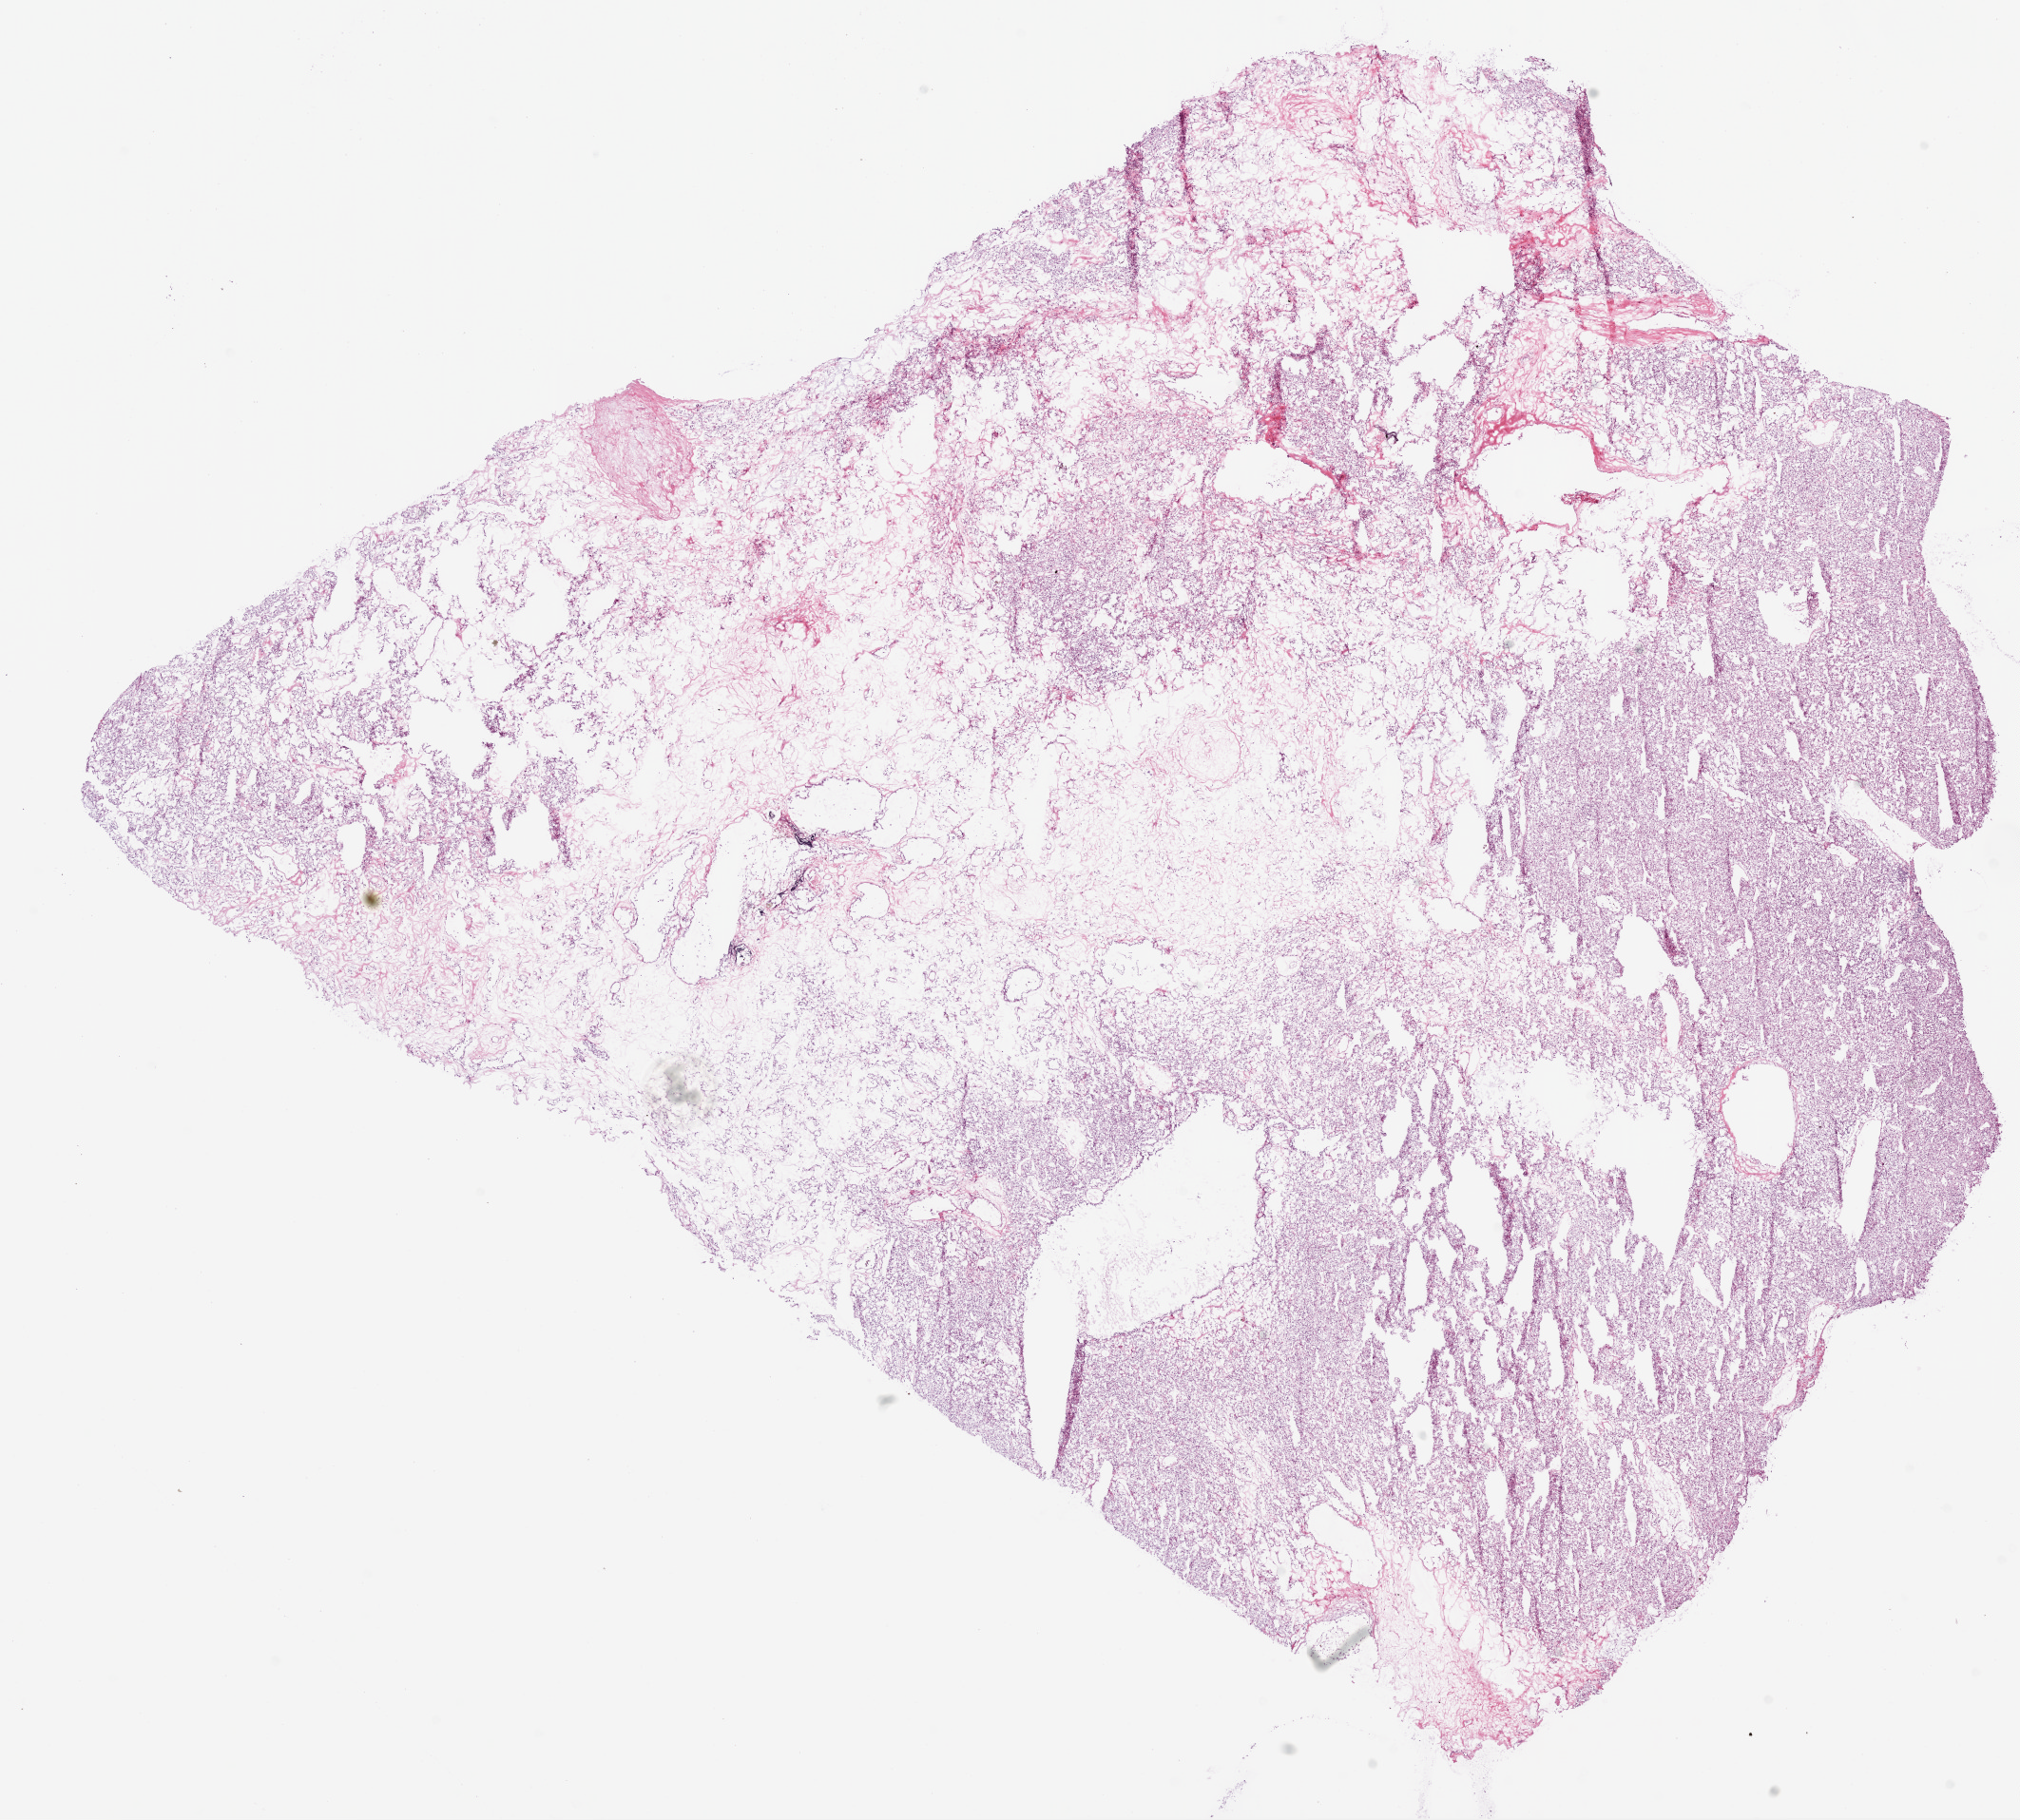
Whole-slide histology image, H&E-stained, low-resolution overview of the scanned area, about 17.1 x 15.4 mm (acquisition: 20x scan), frozen section from the bottom of the tissue portion, sample: primary tumour, kidney. Male, age 64 years at initial diagnosis.
Histologic diagnosis: Clear cell adenocarcinoma, NOS.